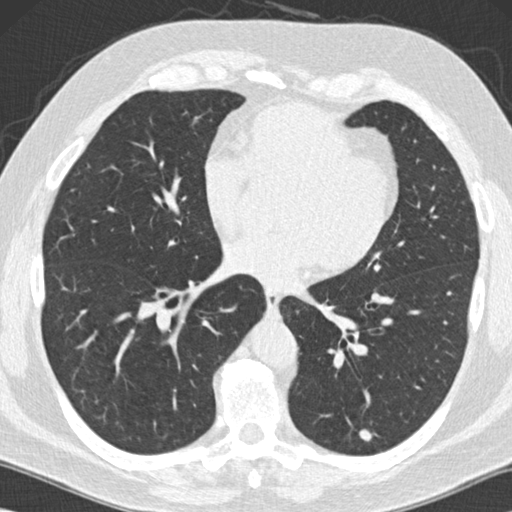
Low-dose screening chest CT, one axial slice. Slice 60 of 152 in the series (ordered by position). 120 kVp. Lung window (W 1500 / L -600 HU). 2 mm slice thickness. 512 × 512 image matrix, field of view 350 × 350 mm.
Outlined on this slice (outlined manually by an expert reader):
- lesion 1 (tumor, lower lobe of left lung): bounding box <359,429,372,441> (left, top, right, bottom; pixels)